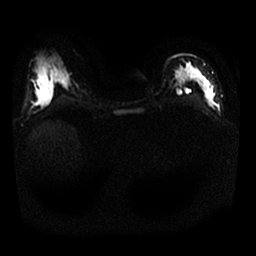
Breast MRI, one axial slice; diffusion-weighted series; image 2 of 4 stored at this slice position (different b-values; order by instance number); 1.5 T; 4 mm slice thickness; 256 × 256 image matrix, field of view 320 × 320 mm. Female patient.
Outlined on this slice (expert manual segmentation):
- tumour on diffusion-weighted imaging: bounding box <197,72,212,105> (left, top, right, bottom; pixels)